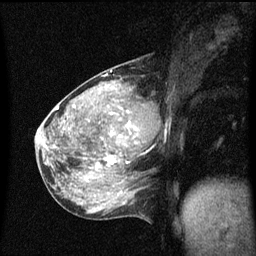
Breast MRI (dynamic contrast-enhanced), one sagittal slice. Slice 22 of 60 in the series (ordered by position). Dynamic contrast-enhanced series, image 2 of 3 at this slice position (ordered by acquisition). 1.5 T. TE 4.2 ms, TR 8.4 ms. 256 × 256 image matrix, field of view 200 × 200 mm. Female patient, age 49 years.
Annotated regions visible in this slice (semi-automatic segmentation, software-assisted and operator-edited):
- analysis volume of interest (the breast-tissue region the enhancement analysis was run in; not a lesion): bounding box <103,90,157,151> (left, top, right, bottom; pixels)
- tumour enhancement mask (voxels above the 70 % enhancement threshold inside the analysis volume of interest): <113,112,136,137>